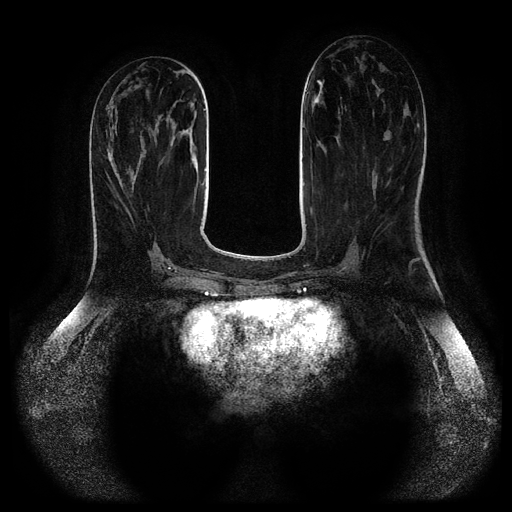
Breast MRI (dynamic contrast-enhanced, multi-phase), one axial slice; slice 39 of 116 in the series (ordered by position); dynamic contrast-enhanced series, time point 2 of 5 at this slice position (early post-contrast); 1.5 T; TE 2.6 ms, TR 5.2 ms; 2 mm slice thickness; 512 × 512 image matrix. Patient: female, 44 years.
Structures marked on this image (semi-automatic segmentation, software-assisted and operator-edited):
- breast lesion (labelled benign in the annotation): bounding box <386,136,389,141> (left, top, right, bottom; pixels)